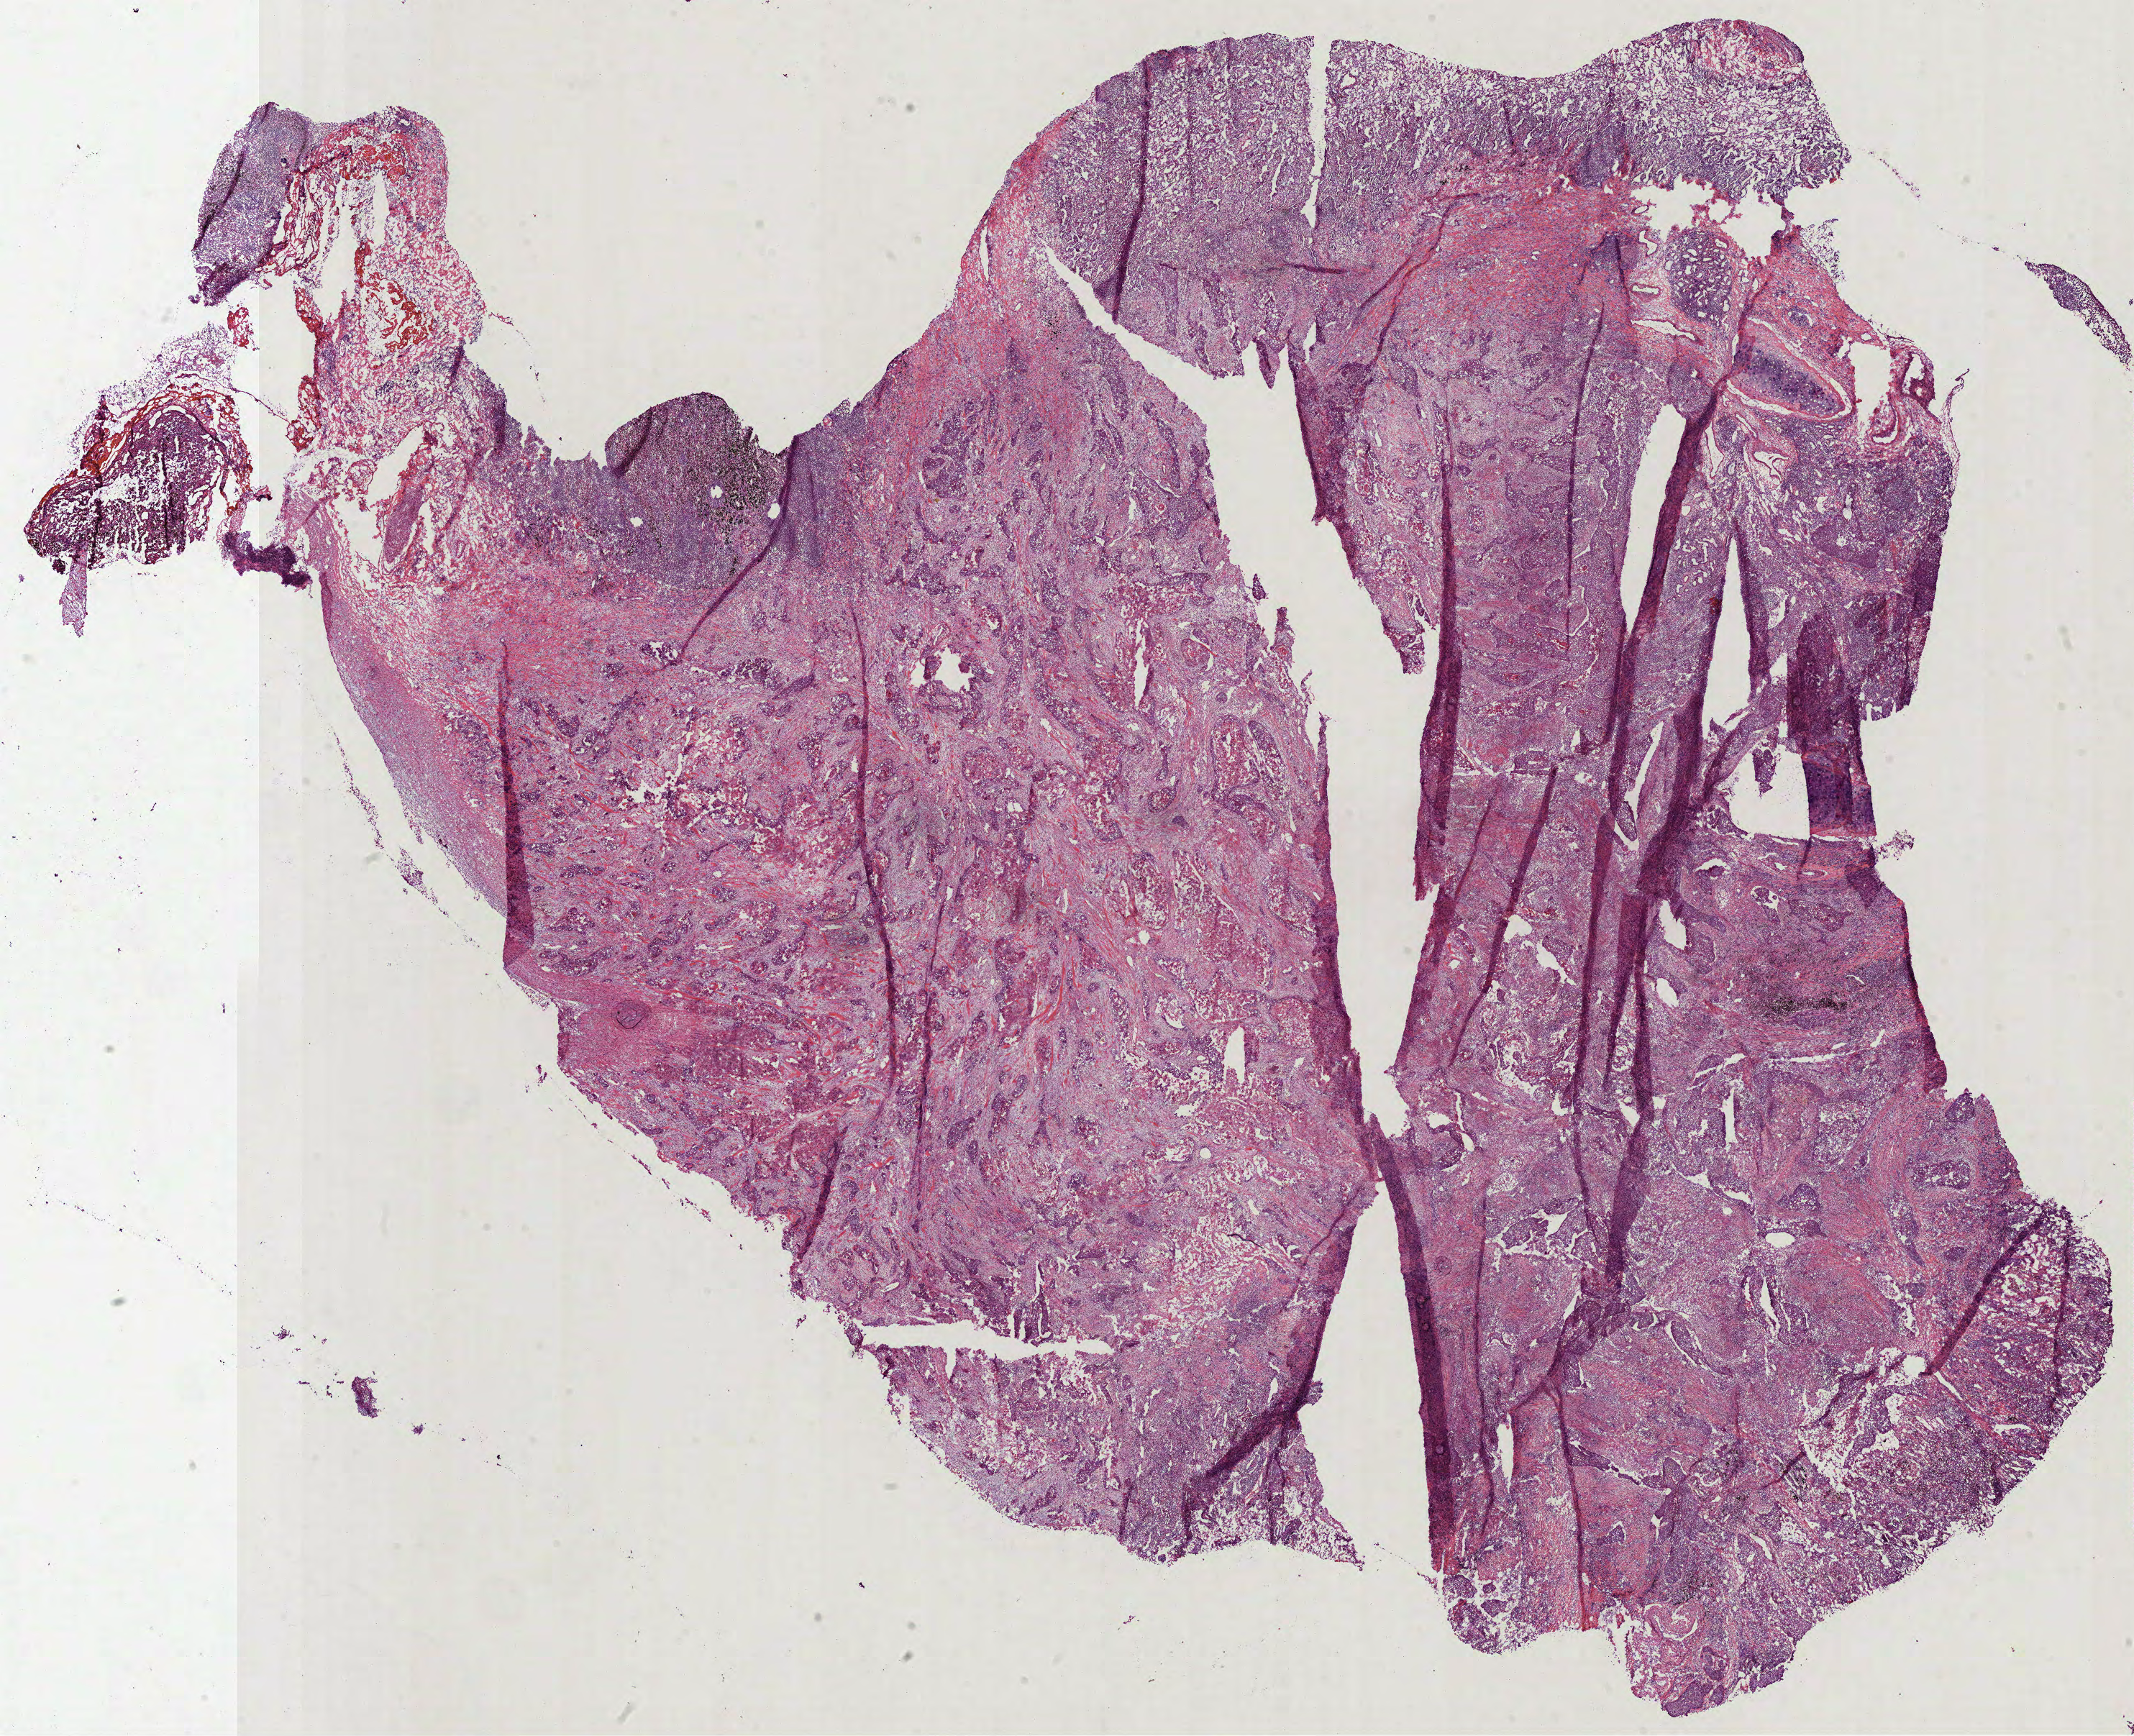
Digitized Hematoxylin and eosin (H&E) stained tissue section (whole slide) — shown as a low-resolution overview of the whole scanned area (about 23.9 x 19.5 mm, slide scanned at 40x). Frozen section. Lung, primary tumour sample. Male patient; age at initial diagnosis 49 years. Pathologist review of this section (percent, as recorded): tumour cells 57%, tumour nuclei 60%, normal cells 8%, stromal cells 30%, necrosis 5%.
TNM: T1a N0 M0. AJCC pathologic stage: IA (7th edition). Diagnosis: Squamous cell carcinoma, keratinizing, NOS (upper lobe, lung).